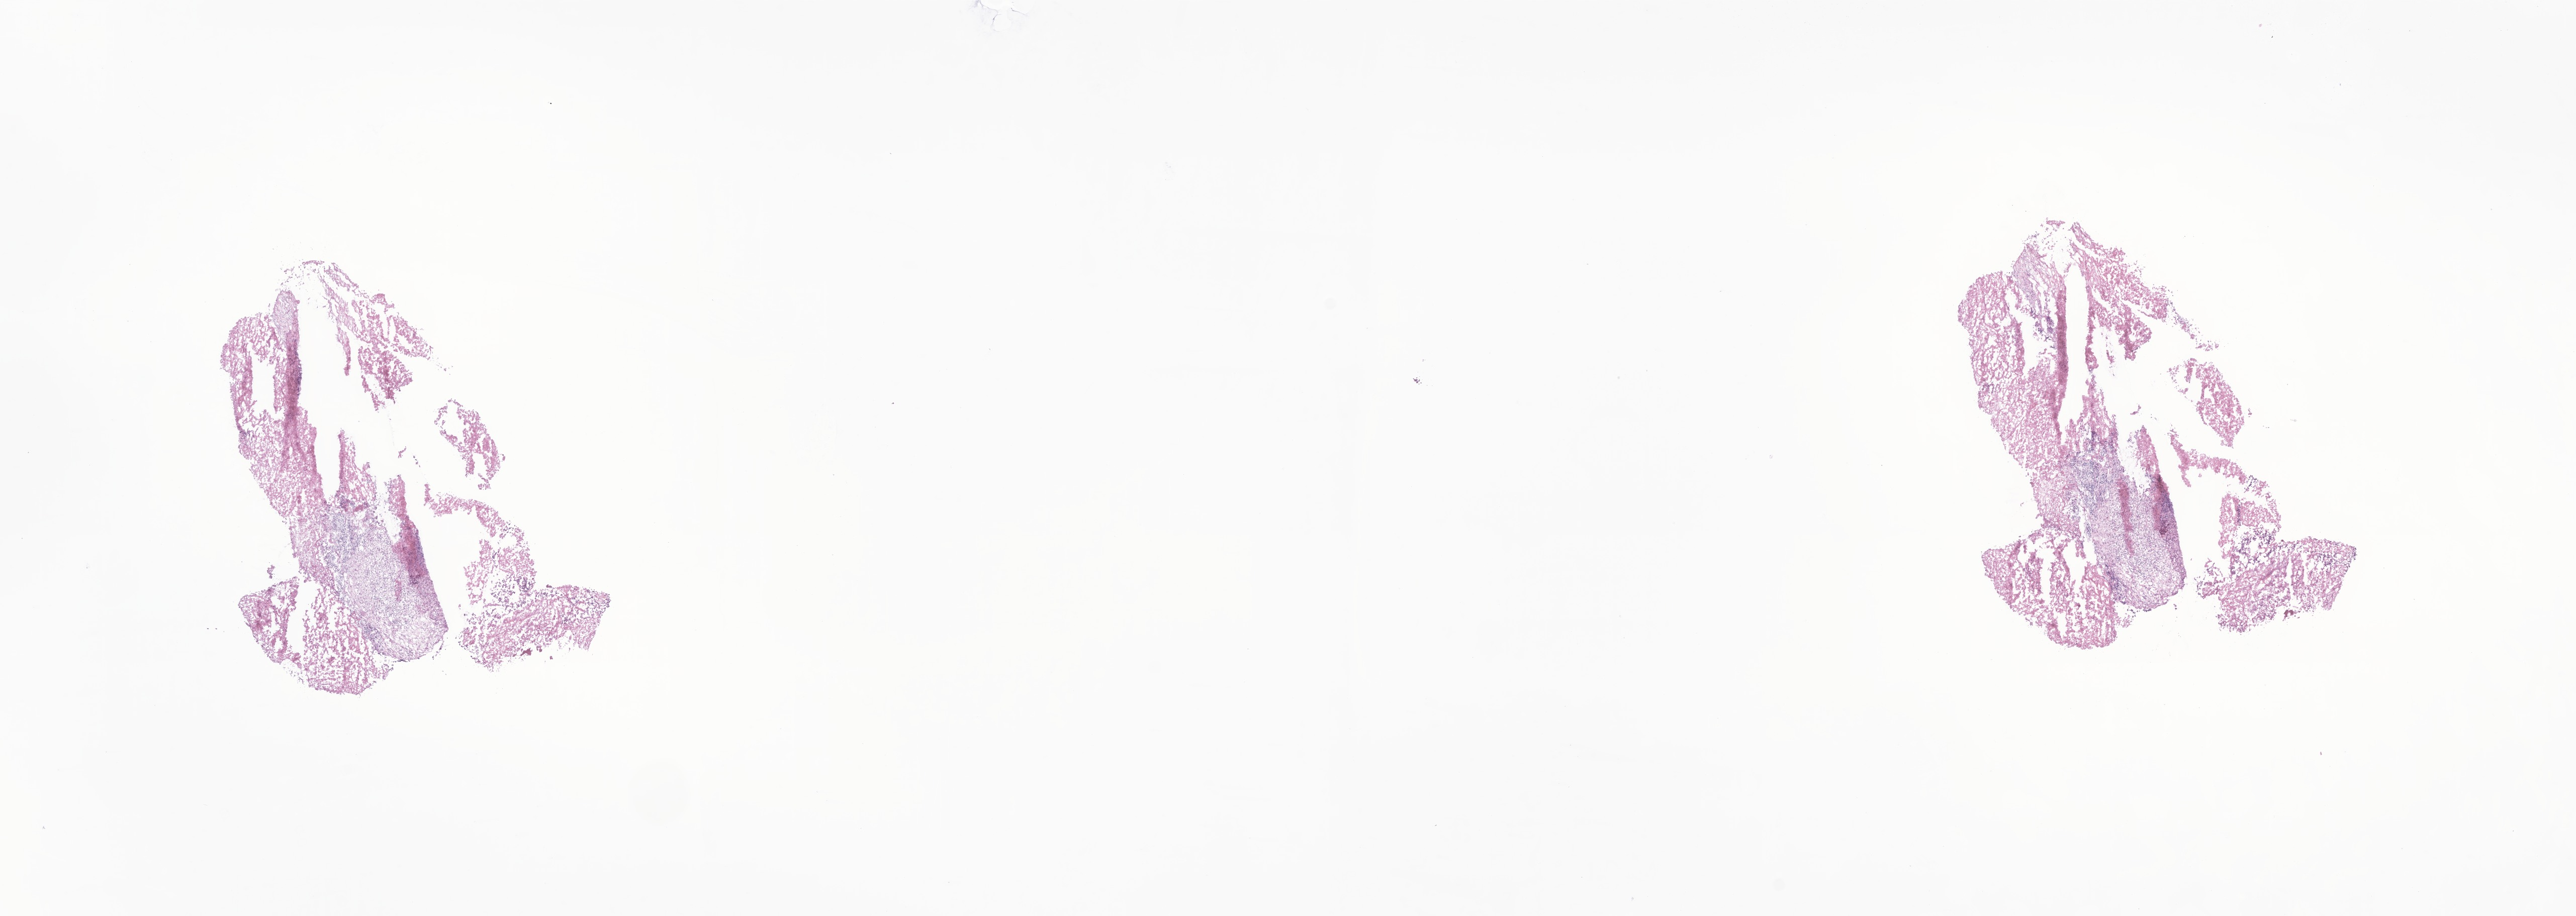
Haematoxylin and eosin whole-slide image of tumor tissue from the adrenal gland — shown as a low-resolution overview of the whole scanned area (about 21.6 x 7.7 mm), frozen section. Female patient, age 462 days (about 1.3 years).
* recorded diagnosis: Neuroblastoma, NOS